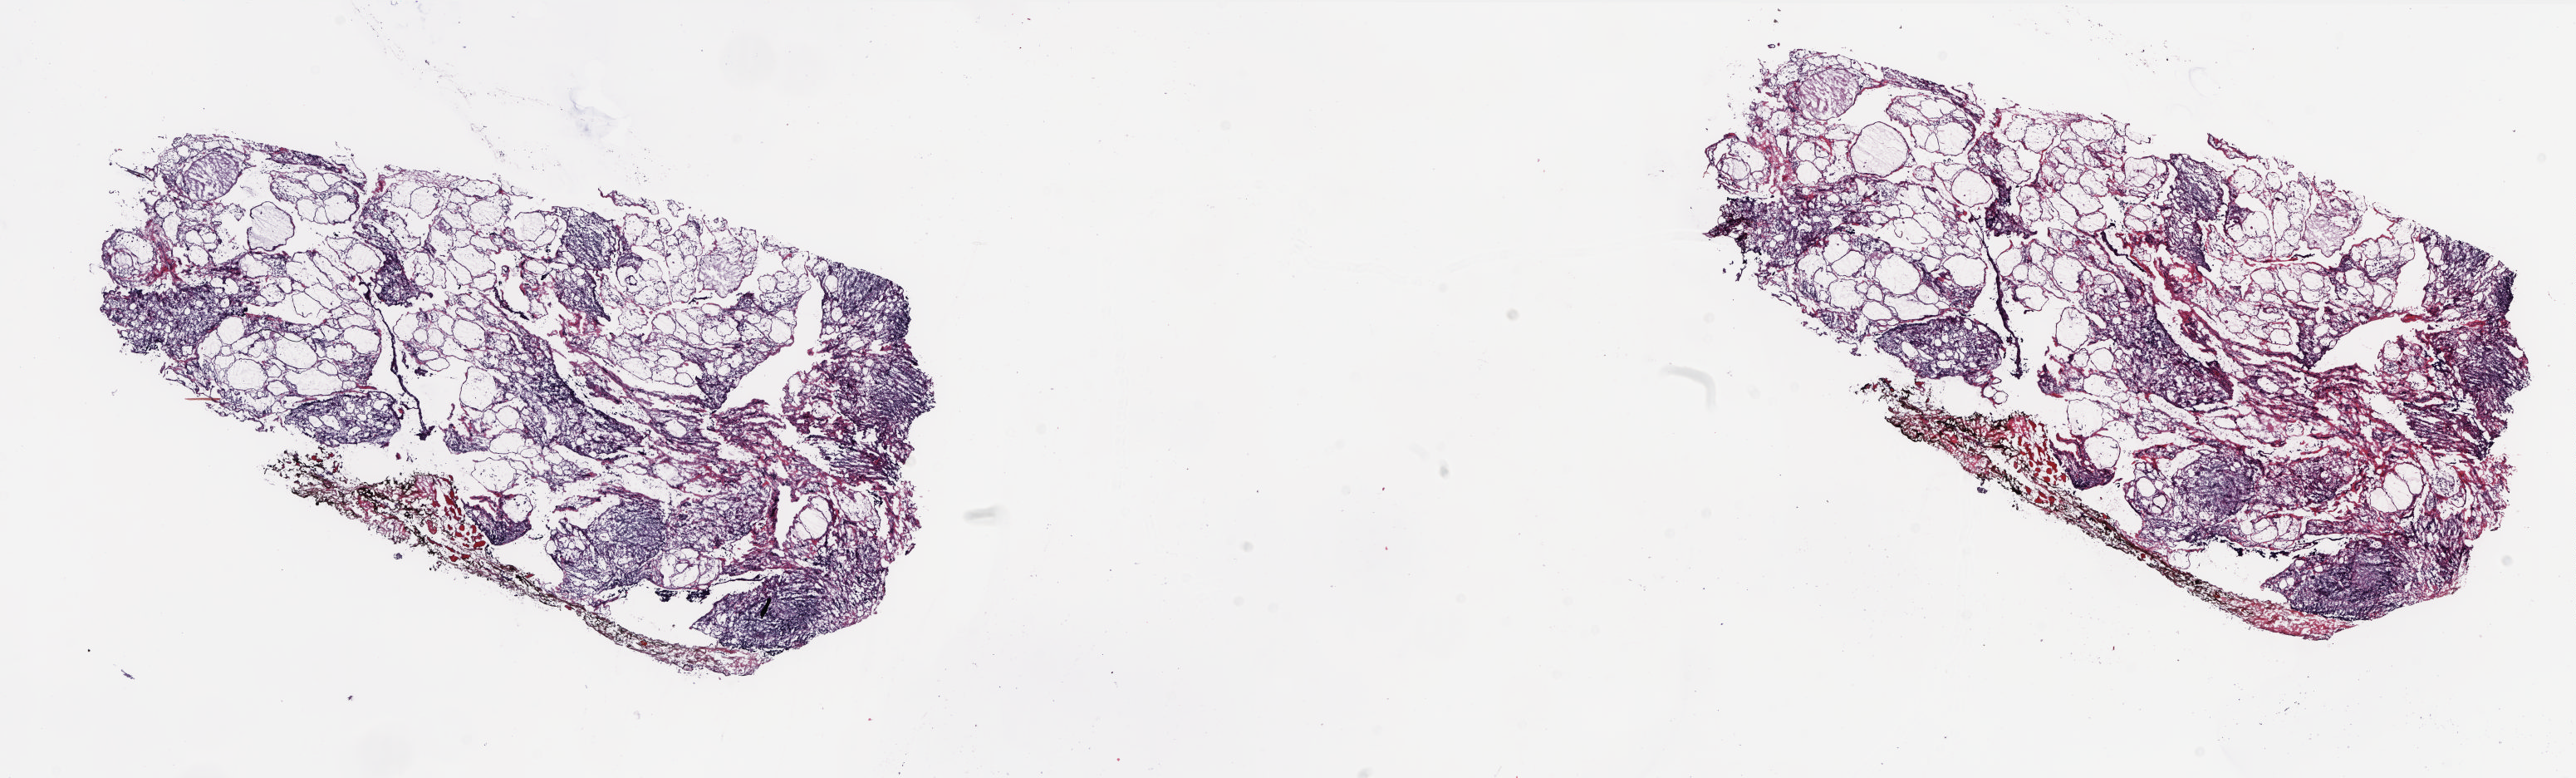
H&E-stained whole-slide image — shown as a low-resolution overview of the whole scanned area (about 25.0 x 7.5 mm, slide scanned at 20x); frozen section from the top of the tissue portion; solid tissue normal (non-tumour tissue) sample from the thyroid. Male, age 47 years at initial diagnosis. Composition of this section per pathologist review: tumour cells 0%, tumour nuclei 0%, normal cells 100%, stromal cells 0%, necrosis 0%. Inflammatory infiltration, as recorded: lymphocyte infiltration 40%, monocyte infiltration 0%, neutrophil infiltration 0%.
* this section: solid tissue normal (non-tumour) sample from the same patient
* patient diagnosis: Papillary adenocarcinoma, NOS (thyroid gland)